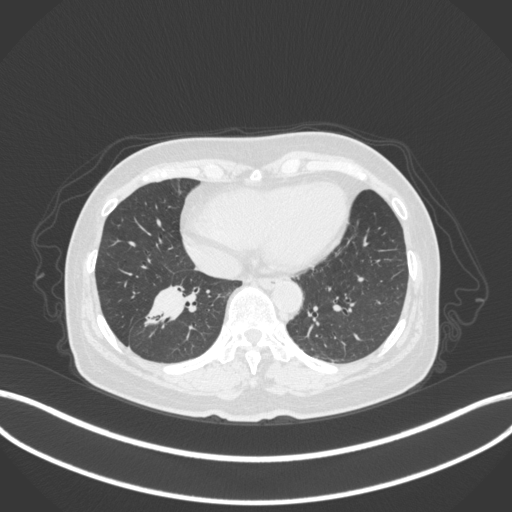
Chest CT, one axial slice; position 129 of 429 along the scan axis; reconstruction kernel B31f; 120 kVp; lung window (W 1500 / L -600 HU); 512 × 512 image matrix. Female patient, age 67 years. Case-level facts recorded for this patient, not image findings: clinical TNM (as recorded): T1c N1 M0; histopathological grade: G2-3.
Outlined on this slice (rectangle marked by the reading radiologist):
- lung tumour (recorded histology: adenocarcinoma): bounding box <140,280,204,328> (left, top, right, bottom; pixels)